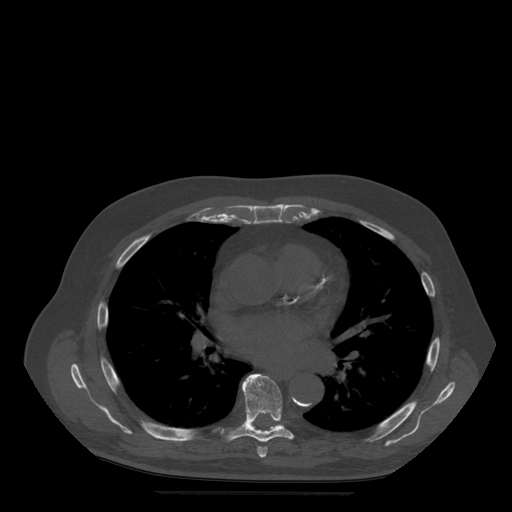
CT including the spine, one axial slice; slice 335 of 522 in the series (ordered by position); bone window (W 1800 / L 400 HU); 1.25 mm slice thickness; 512 × 512 image matrix. Patient age 72 years. Case-level facts recorded for this patient, not image findings: primary cancer: prostate.
Structures marked on this image (semi-automatic segmentation, software-assisted and operator-edited):
- T6 vertebra: bounding box [x1, y1, x2, y2] px = [243, 384, 268, 458]
- T7 vertebra: [222, 374, 294, 443]
- T8 vertebra: [251, 424, 255, 428]